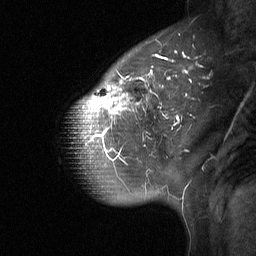
Breast MRI (dynamic contrast-enhanced), one sagittal slice. Slice 47 of 64 in the series (ordered by position). Dynamic contrast-enhanced study with each time point stored as its own series, time point 2 of 3 at this slice position (early post-contrast, ordered by acquisition time). 1.5 T. TE 4.8 ms, TR 27 ms. 2 mm slice thickness. 256 × 256 image matrix, field of view 200 × 200 mm. Patient: female, 42 years. From the clinical record (not read from this slice): setting: breast cancer imaged before/during neoadjuvant chemotherapy; receptor status: triple-negative.
Structures marked on this image (semi-automatically segmented with operator editing):
- analysis volume of interest (the breast-tissue region the enhancement analysis was run in; not a lesion): bounding box (x1, y1, x2, y2) in pixels: (69, 31, 203, 190)
- tumour enhancement mask (voxels above the 90 % enhancement threshold inside the analysis volume of interest): (85, 53, 185, 154)